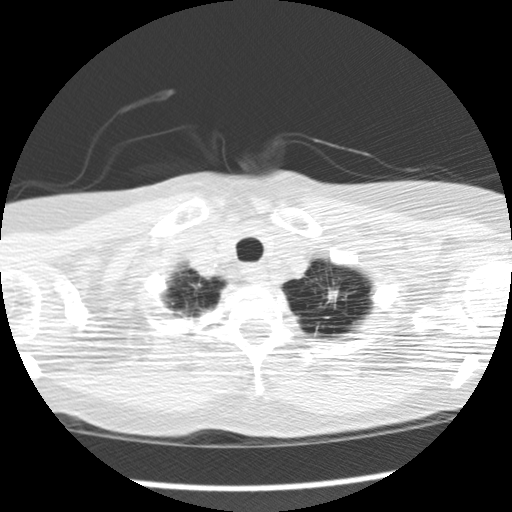
Axial slice from a low-dose chest CT screening exam; second annual screen; lung window (W 1500 / L -600 HU); 2.5 mm slice thickness; 512 × 512 image matrix, field of view 308 × 308 mm. Female, age 69 years at enrolment. Former smoker at enrolment.
Expert reader's lesion annotation, bounding box [x1, y1, x2, y2] px = [311, 275, 364, 322]. The screening reader recorded 2 non-calcified nodules or masses ≥4 mm on this exam (right upper lobe, lingula); which of them this box marks is not recorded. Participant outcome: lung cancer diagnosed 147 days after this screen — adenocarcinoma, NOS, left upper lobe, poorly differentiated (G3), stage IB (AJCC 6th edition), 80 mm at pathology.